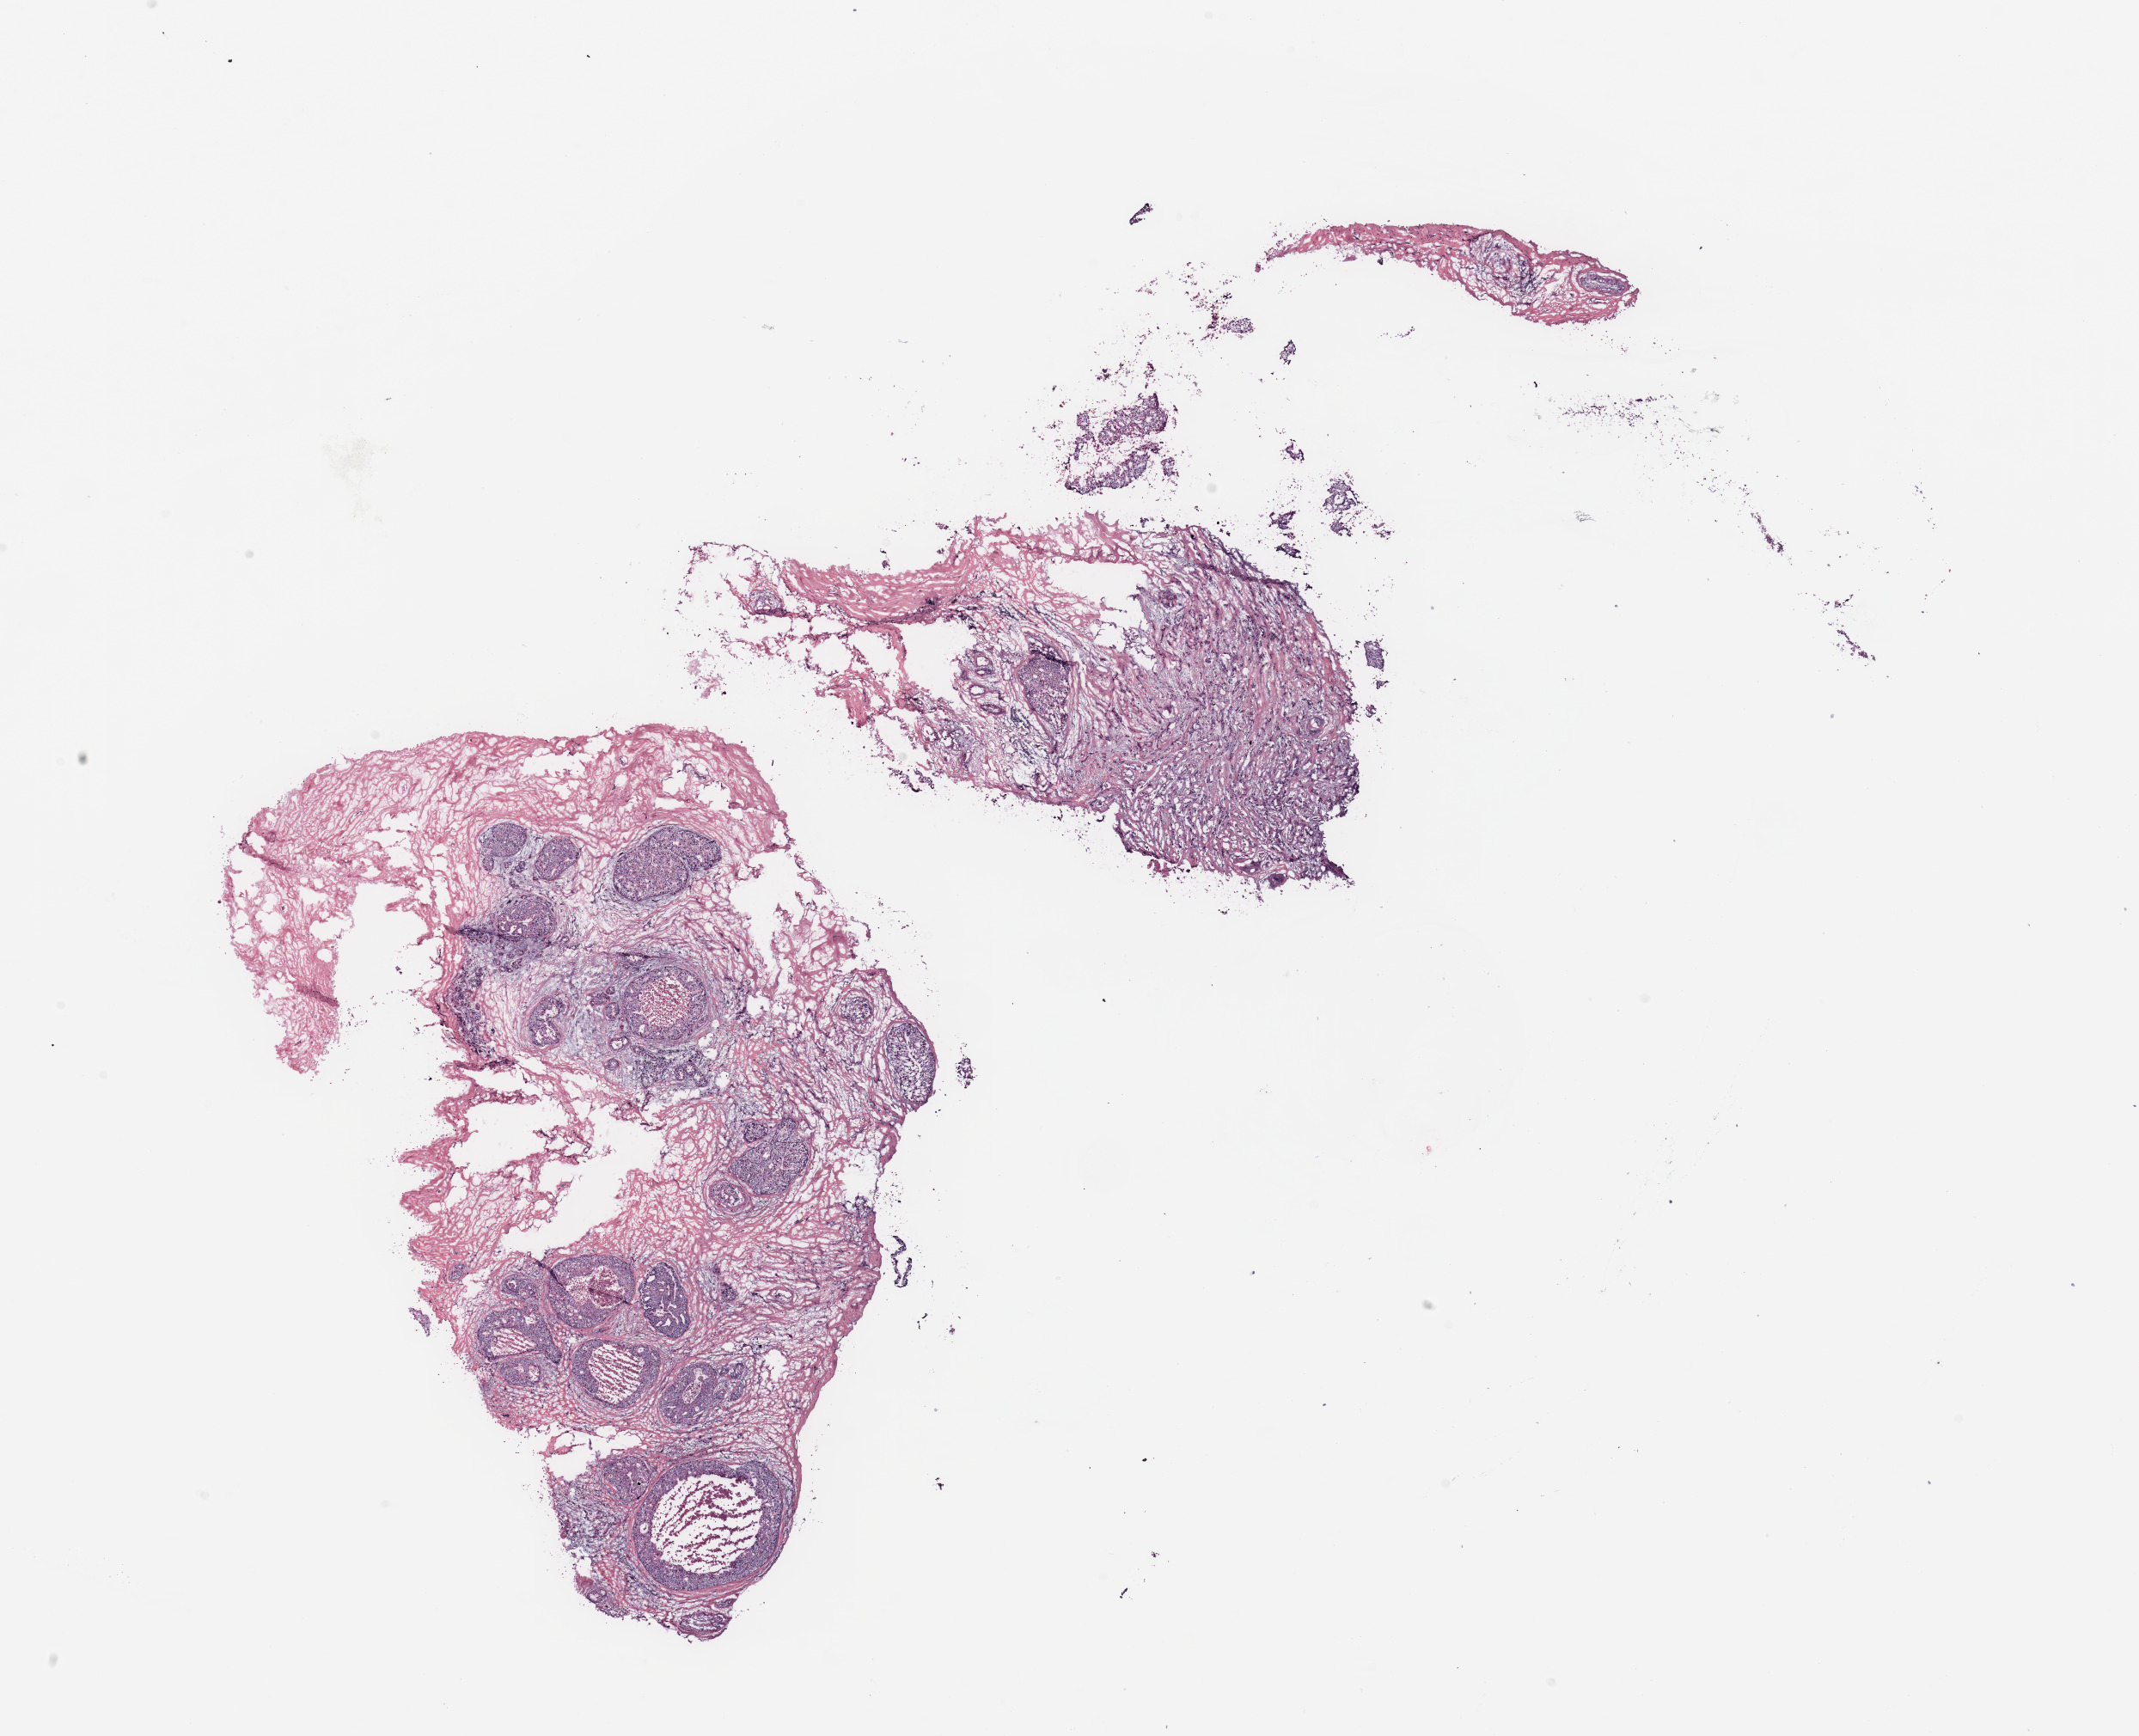
H&E-stained whole-slide image — a low-resolution overview of the entire scanned area, about 19.7 x 16.0 mm (acquisition: 20x scan), breast, tissue type not recorded.
* patient diagnosis (cohort enrolment): breast cancer (breast)